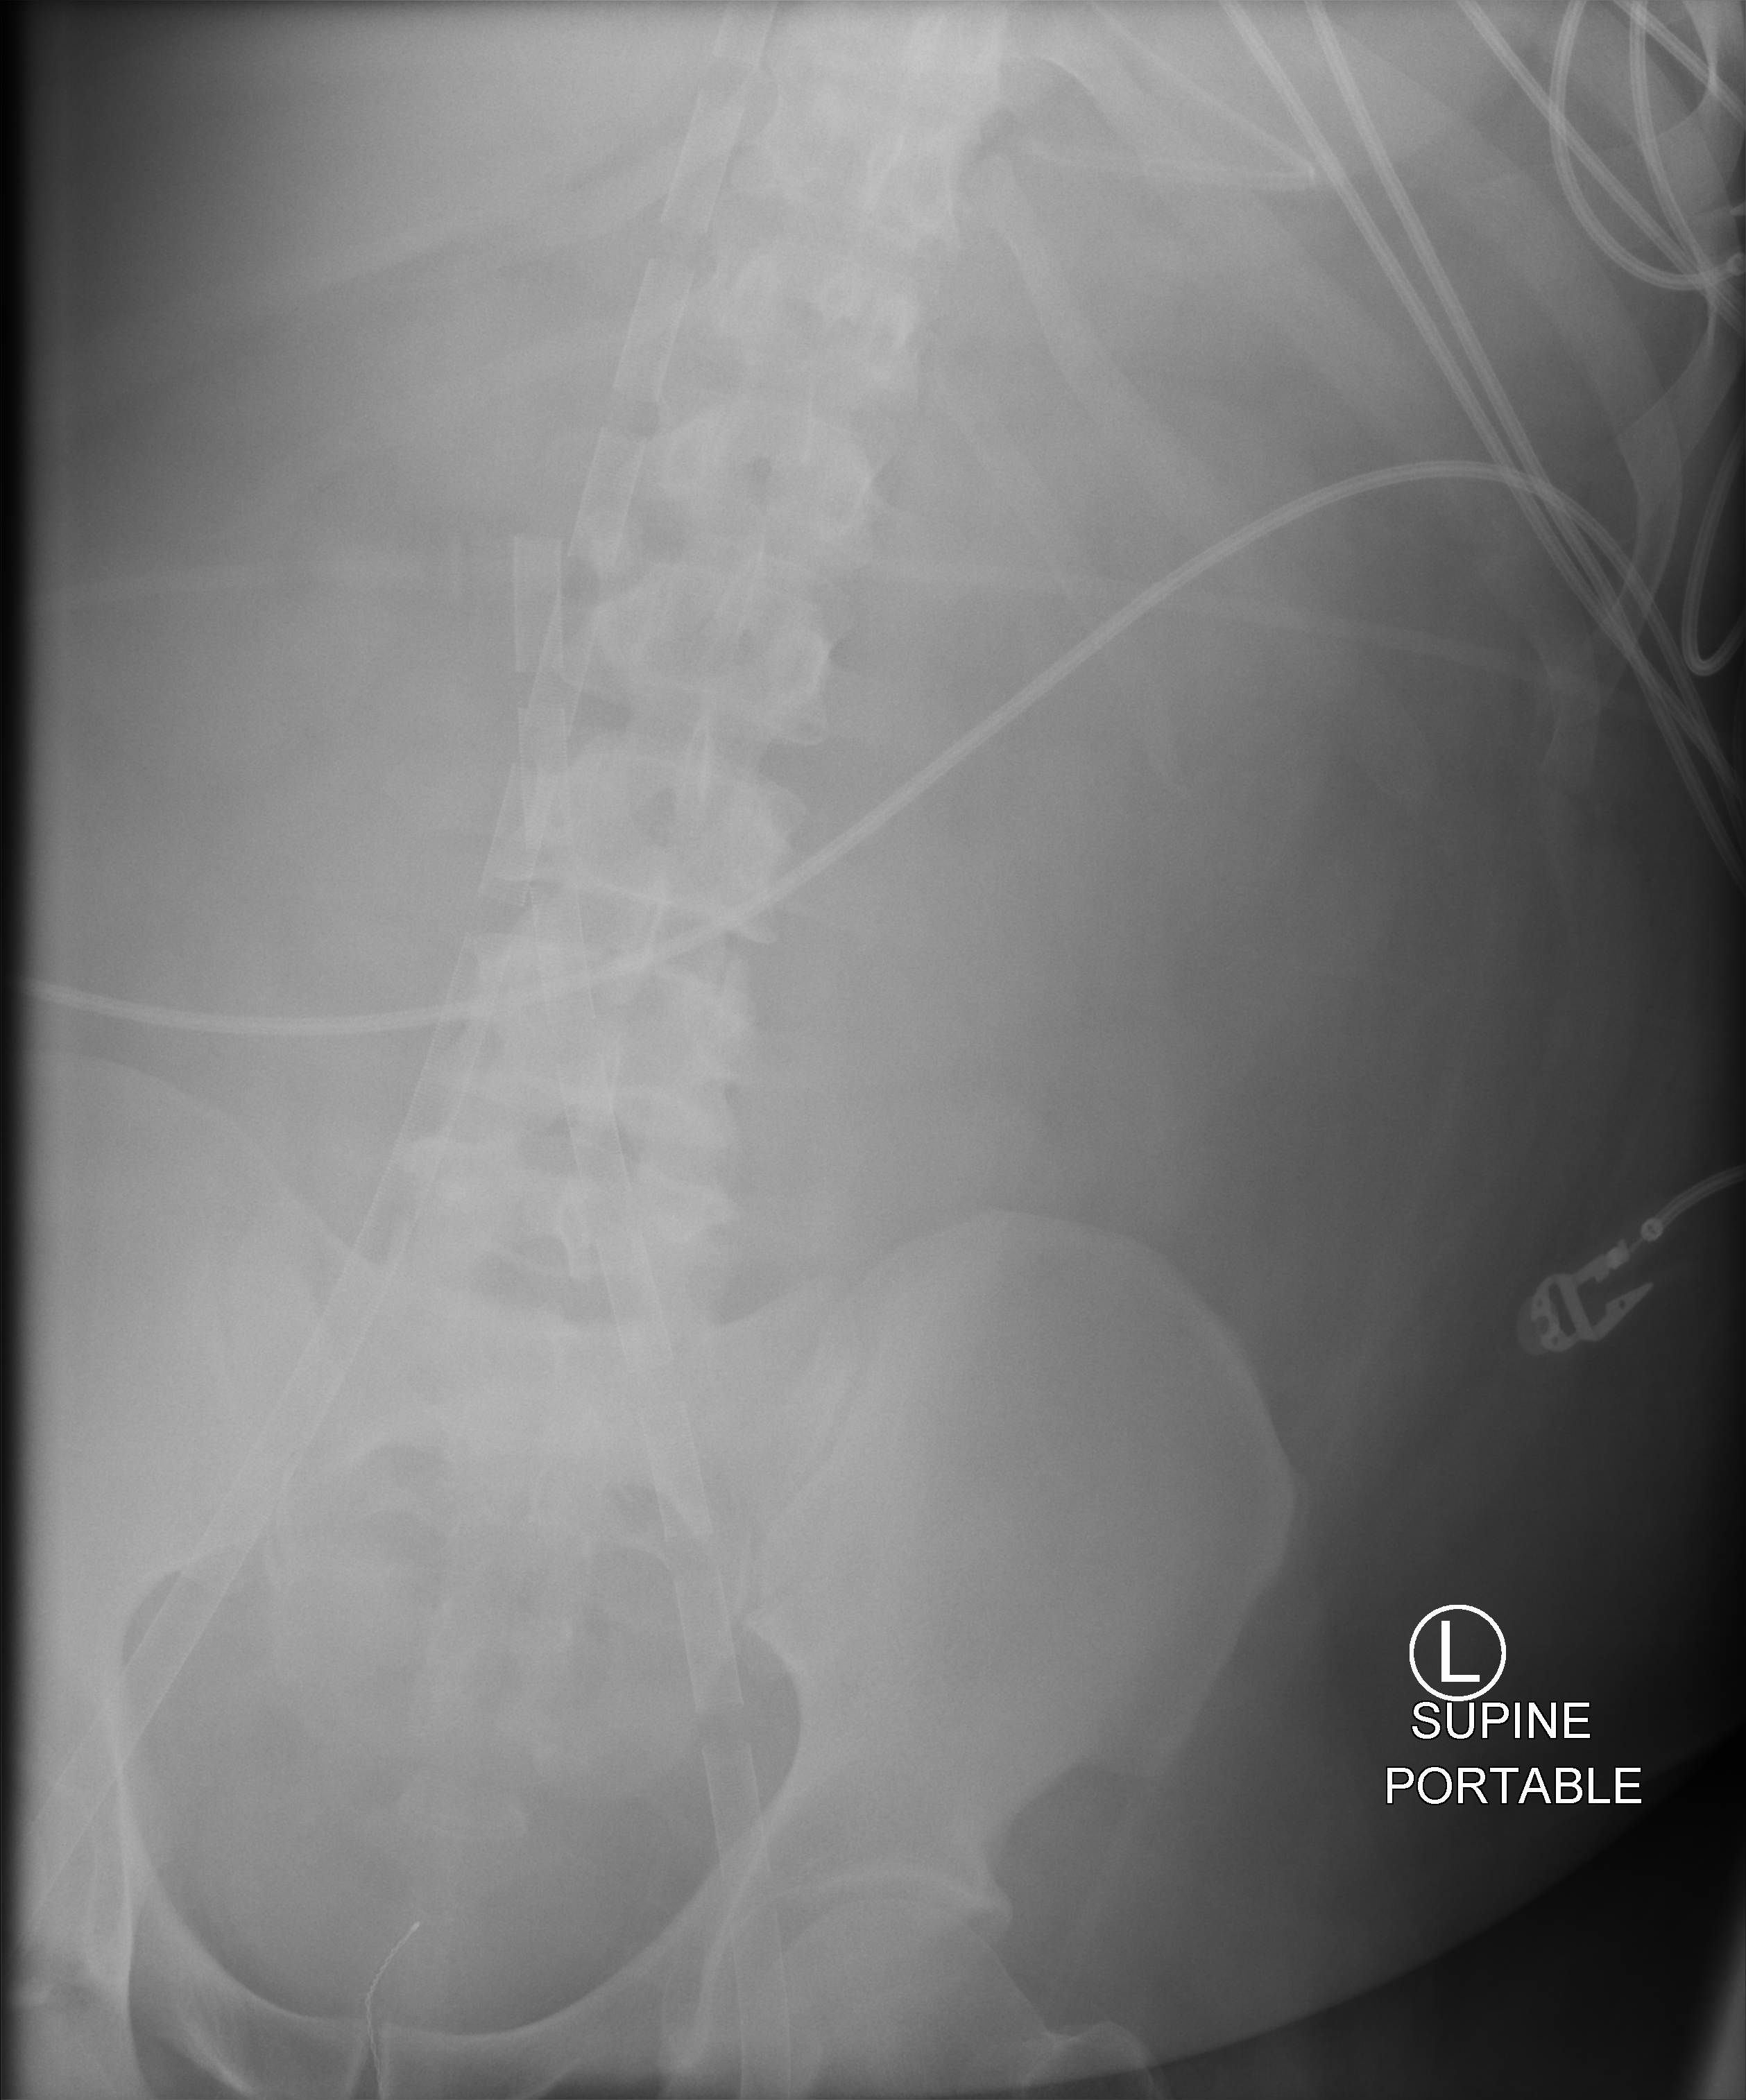
Abdomen X-ray (portable), anteroposterior (AP) projection. Patient hospitalised with COVID-19, aged 18–59 years.
From the hospital-stay record, not from the radiograph (when in the stay this image was taken is not recorded):
- admitted to intensive care during this hospital stay: yes